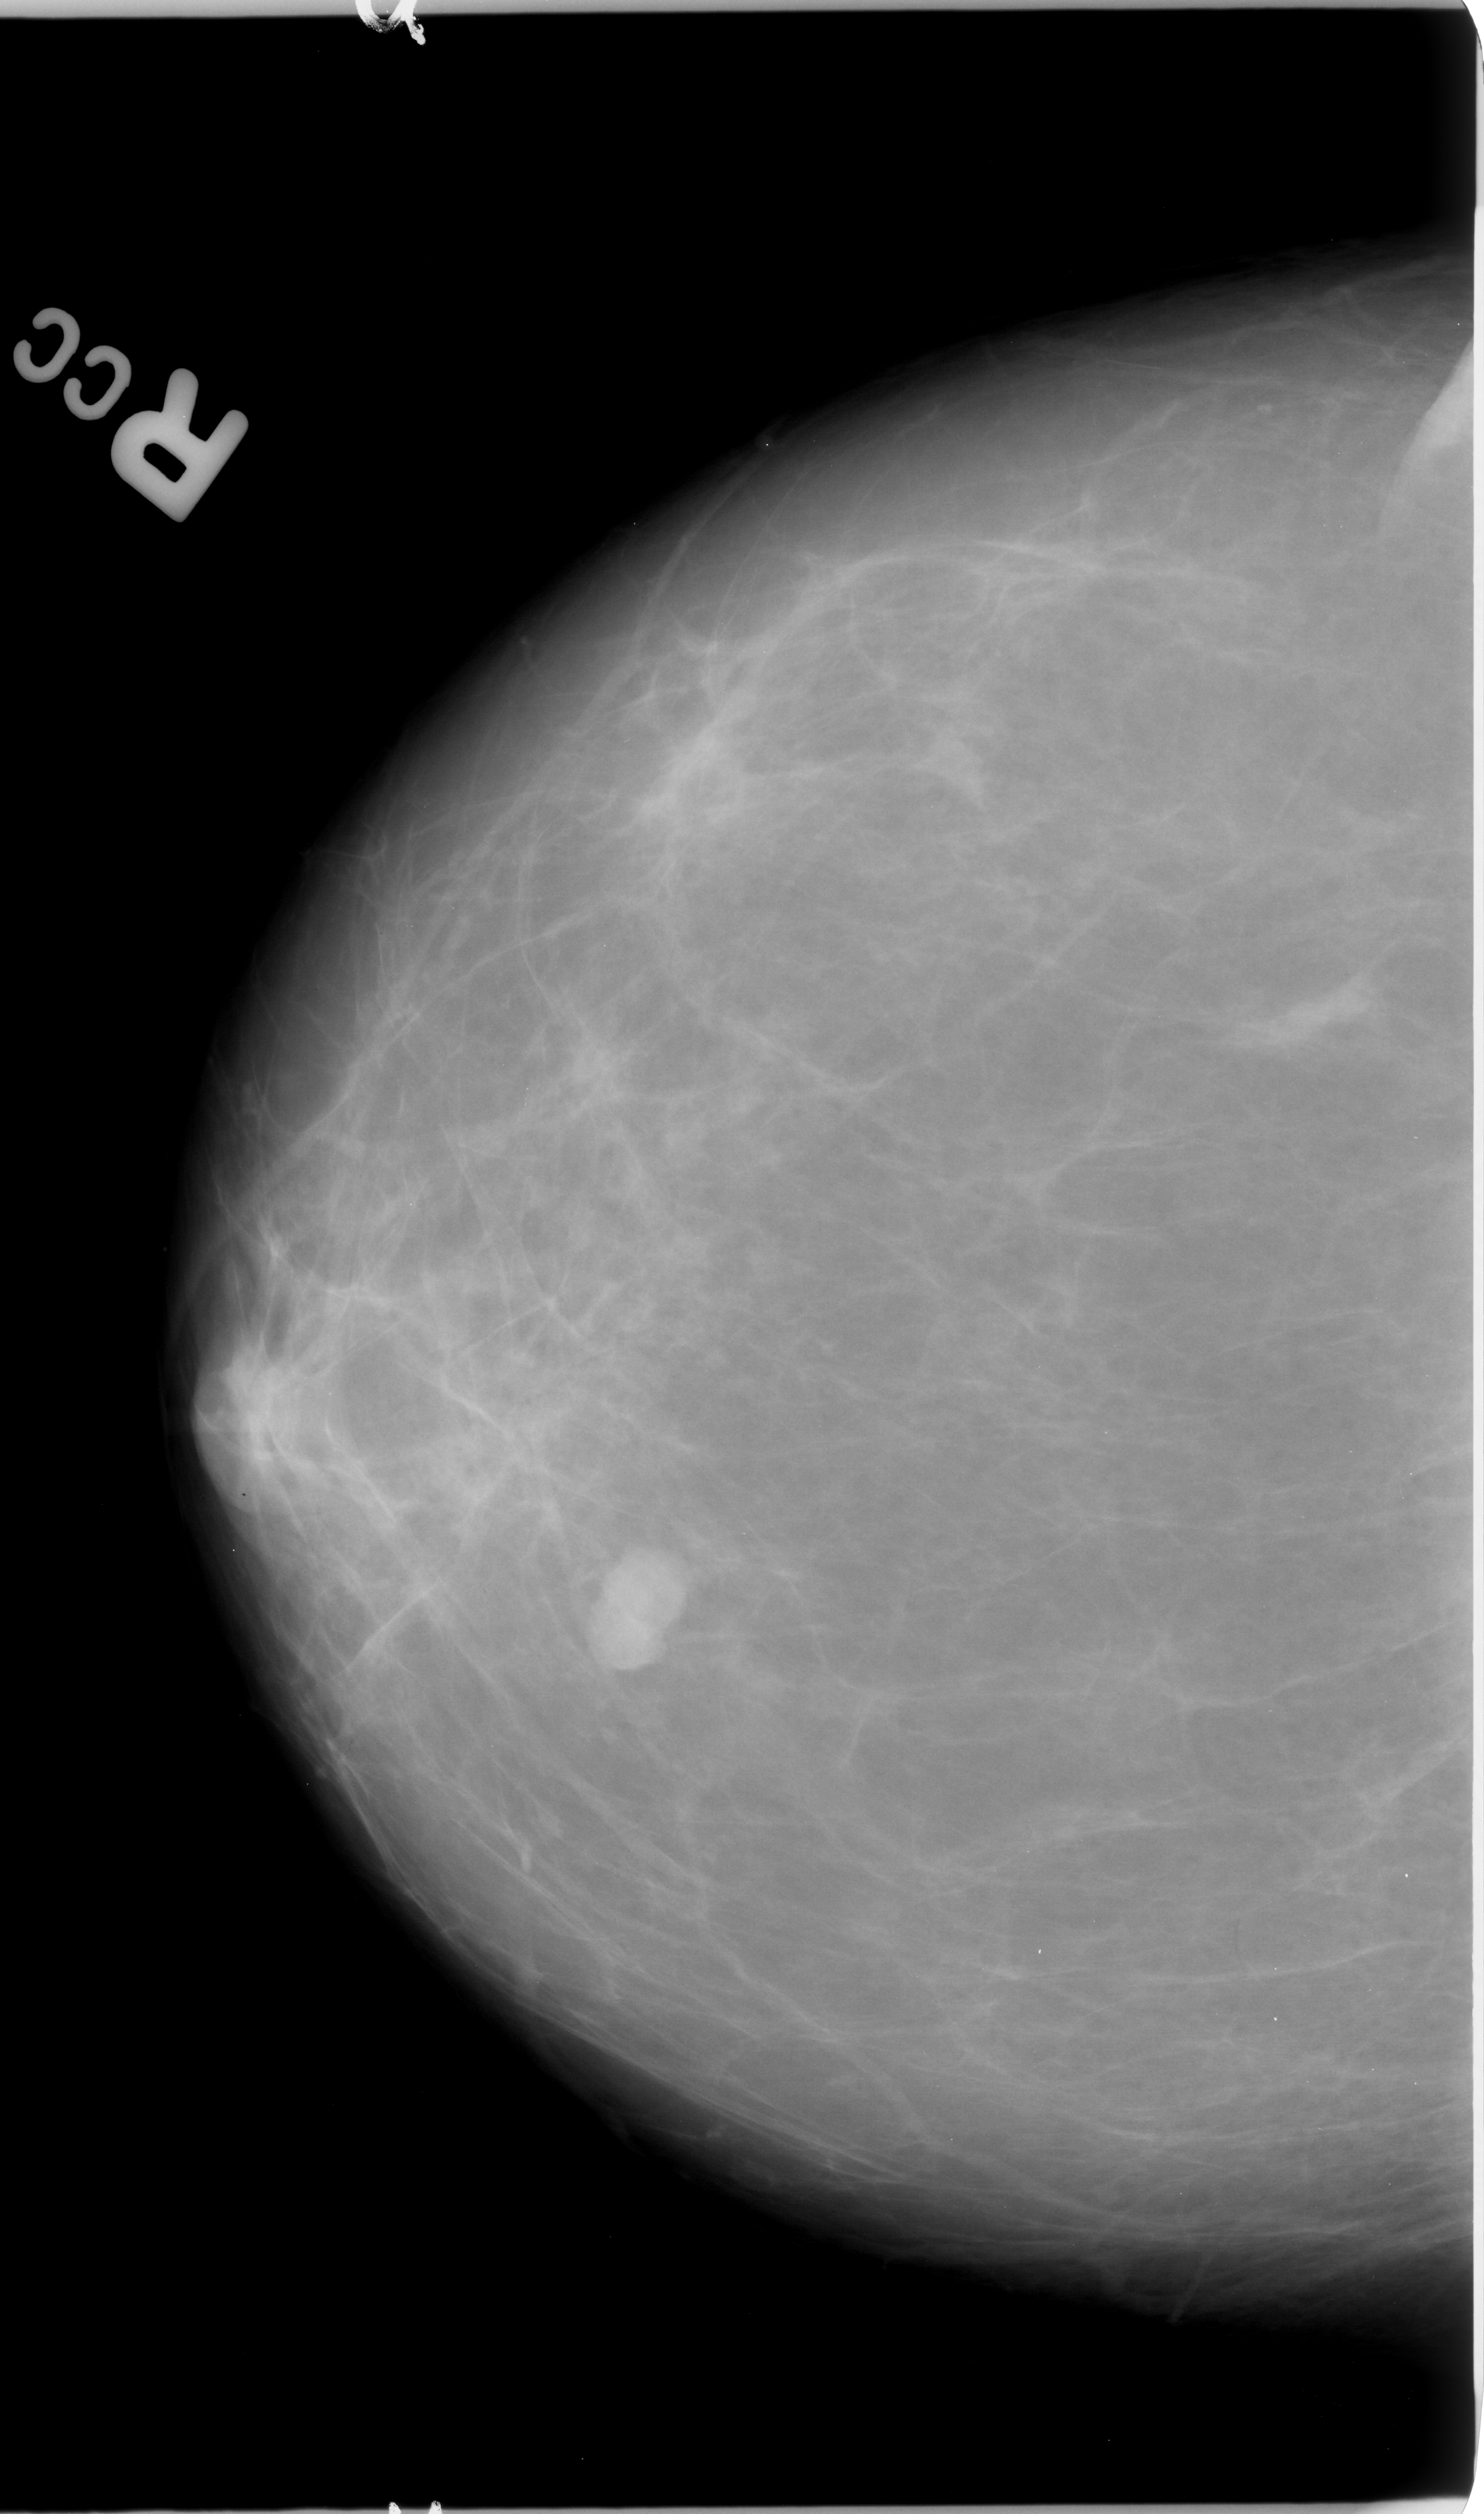
Digitized screen-film mammogram. Right breast. Craniocaudal (CC) view. BI-RADS breast density category 1 (scale 1–4). 1484 × 2514 image matrix.
Marked abnormalities (boxes around the expert regions of interest):
- mass, shape lobulated, margins circumscribed / ill defined; BI-RADS assessment category 4; subtlety rating 5 on a 1 (subtle) to 5 (obvious) scale; pathology result (as recorded, not read from the image): malignant: bounding box [x1, y1, x2, y2] px = [570, 1543, 704, 1689]